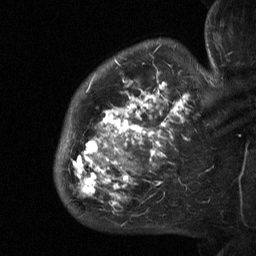
Breast MRI (dynamic contrast-enhanced), one sagittal slice; position 48 of 64 along the scan axis; dynamic contrast-enhanced study with each time point stored as its own series, time point 2 of 3 at this slice position (early post-contrast, ordered by acquisition time); 1.5 T; TE 4.8 ms, TR 27 ms; 2.3 mm slice thickness; 256 × 256 image matrix, field of view 200 × 200 mm. Female patient, age 50 years. From the clinical record (not read from this slice): setting: breast cancer imaged before/during neoadjuvant chemotherapy; receptor status: HER2-positive.
Annotated regions visible in this slice (semi-automatically segmented with operator editing):
- analysis volume of interest (the breast-tissue region the enhancement analysis was run in; not a lesion): box from (x=54, y=64) to (x=211, y=218) px
- tumour enhancement mask (voxels above the 90 % enhancement threshold inside the analysis volume of interest): (x=72, y=72)–(x=189, y=206)